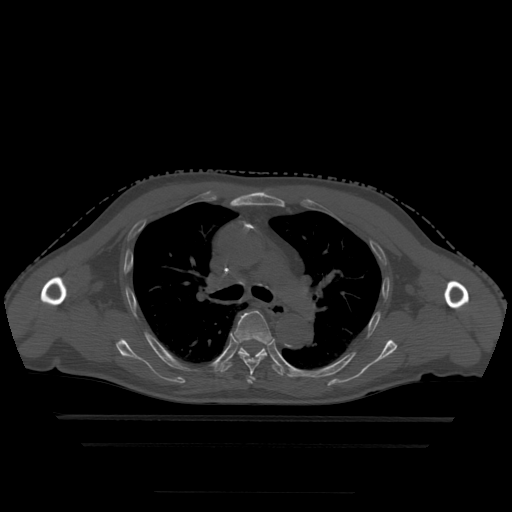
CT including the spine, one axial slice. Bone window (W 1800 / L 400 HU). 512 × 512 image matrix, field of view 436 × 436 mm. Patient age 68 years. Case-level facts recorded for this patient, not image findings: primary cancer: urothelial.
Outlined on this slice (semi-automatic segmentation, software-assisted and operator-edited):
- T4 vertebra: box from (x=248, y=382) to (x=251, y=384) px
- T5 vertebra: (x=234, y=311)–(x=273, y=384)
- T6 vertebra: (x=220, y=338)–(x=284, y=376)